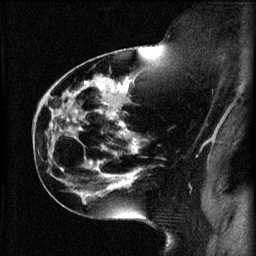
Breast MRI (dynamic contrast-enhanced), one sagittal slice; position 34 of 60 along the scan axis; 3 images stored at this slice position (order not interpretable as contrast timing); 1.5 T; TE 4.2 ms, TR 11 ms; 2 mm slice thickness; 256 × 256 image matrix. Female patient, age 44 years.
Outlined on this slice (semi-automatic segmentation, software-assisted and operator-edited):
- analysis volume of interest (the breast-tissue region the enhancement analysis was run in; not a lesion): bounding box [x1, y1, x2, y2] px = [110, 124, 145, 179]
- tumour enhancement mask (voxels above the 70 % enhancement threshold inside the analysis volume of interest): [112, 124, 143, 179]